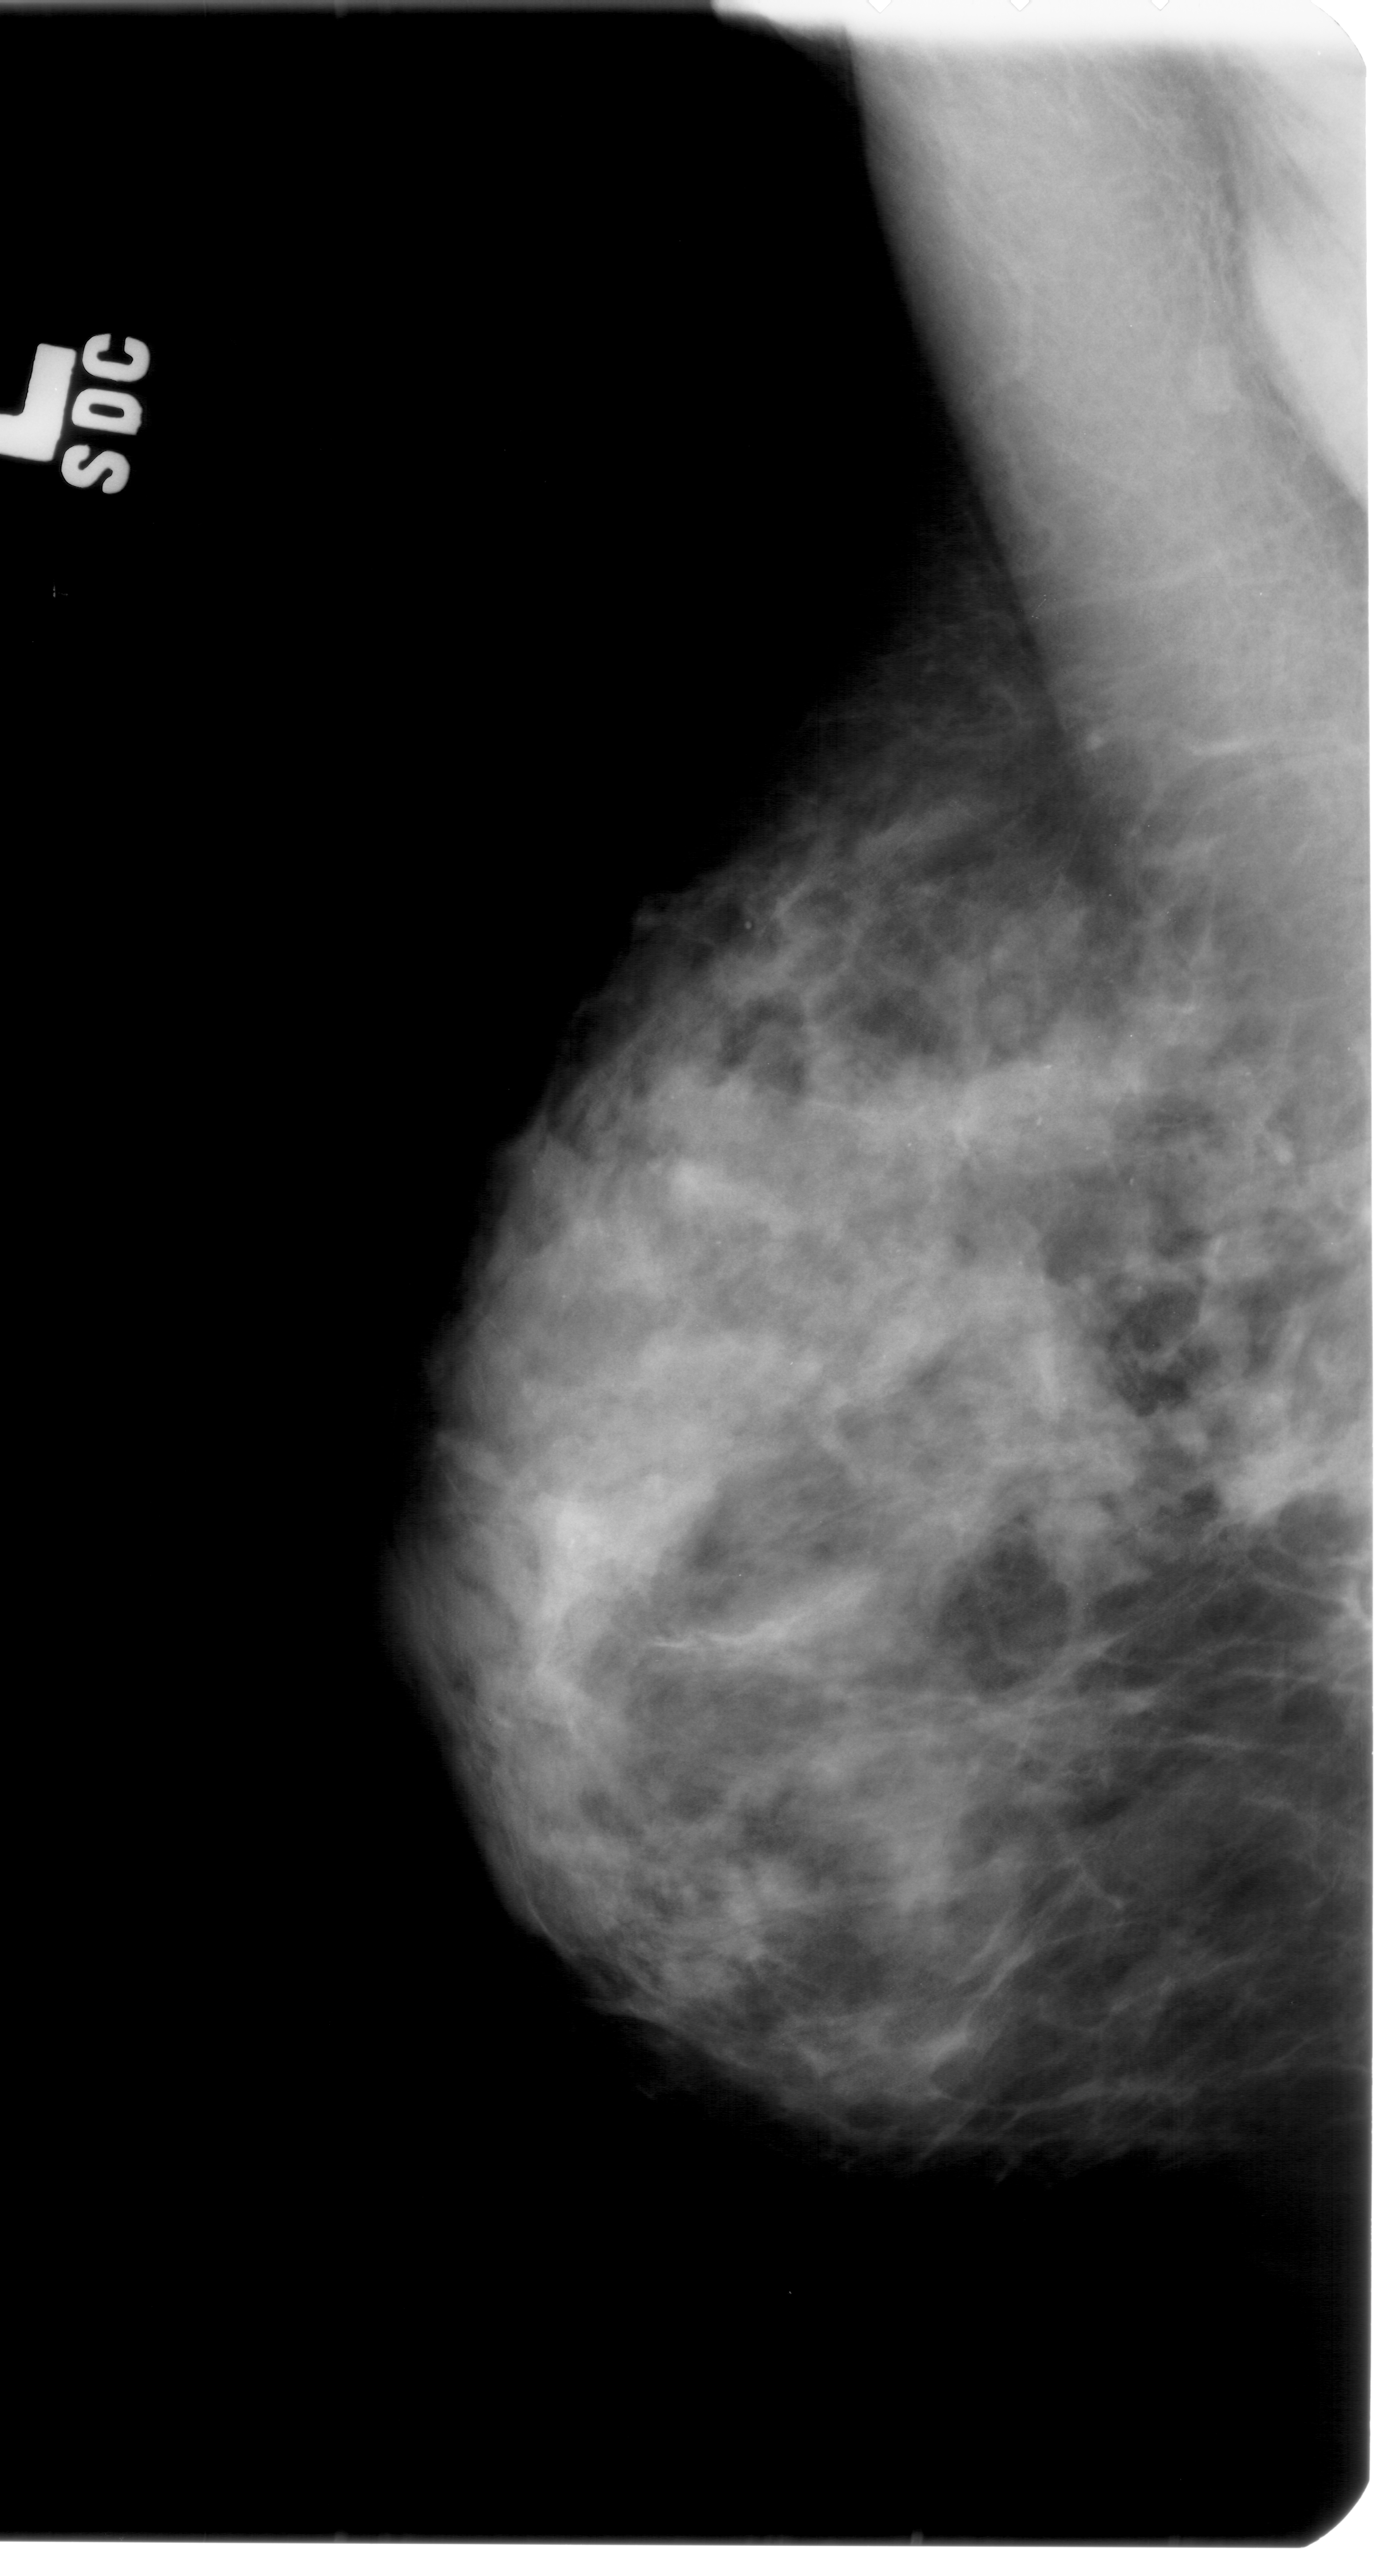
Scanned film-screen mammogram. Left breast. MLO view. BI-RADS breast density category 3 (scale 1–4). 1383 × 2576 image matrix.
Expert-marked regions of interest on this film, with their recorded descriptors:
- calcifications, morphology pleomorphic, distribution segmental; BI-RADS assessment category 4; pathology (as recorded): malignant: bounding box (x1, y1, x2, y2) in pixels: (490, 980, 1368, 1602)